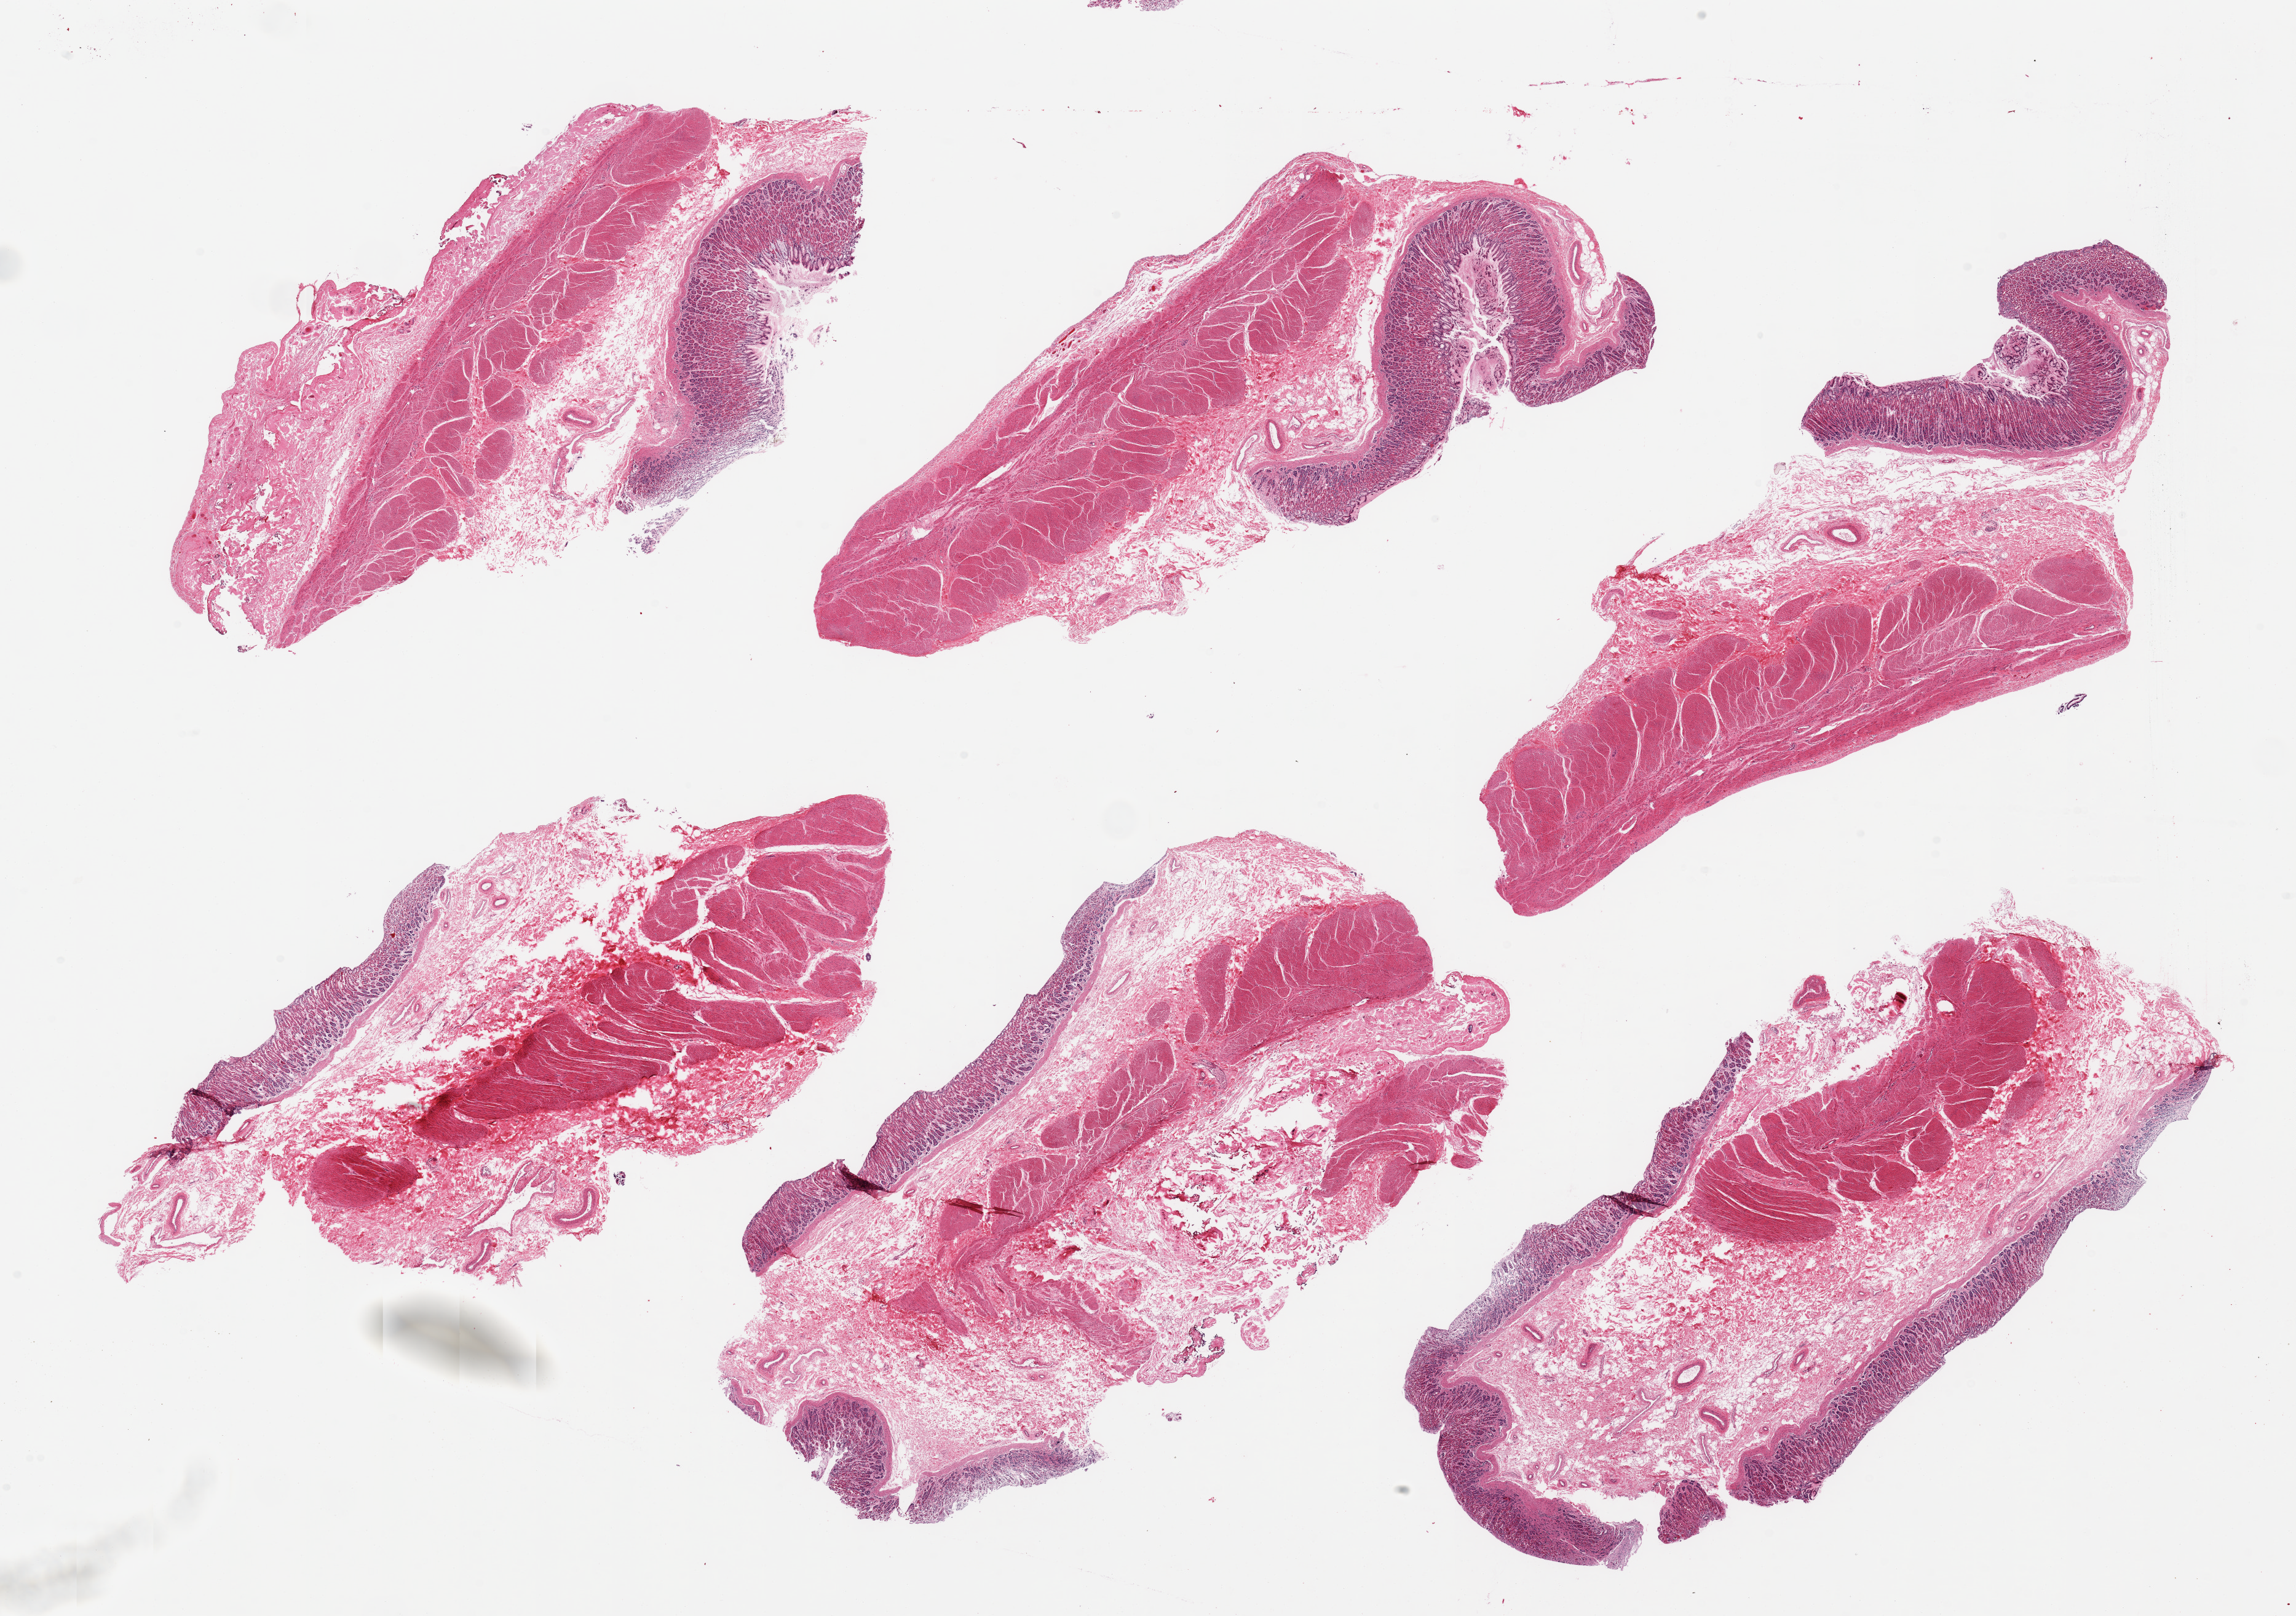
Digitized haematoxylin and eosin-stained section, whole scanned area (about 29.5 x 20.8 mm, acquisition: 20x scan) shown as a low-resolution overview. PAXgene-fixed, paraffin-embedded tissue. Sampled site (target tissue): stomach. Donor tissue sample. Male donor.
Review note (as recorded): 6 pieces; full thickness sections.